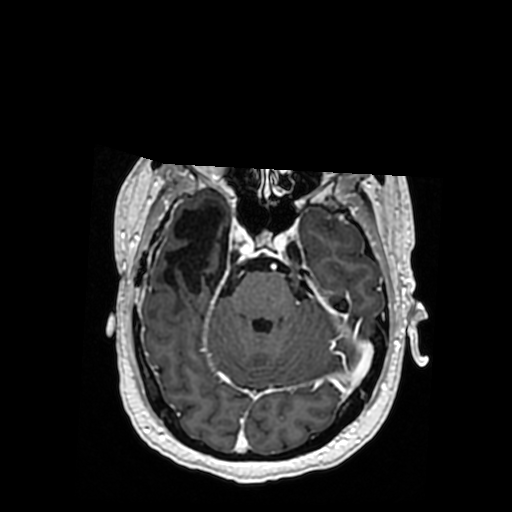
Brain MRI from a brain-tumour surgery series, one axial slice. Slice 239 of 364 in the series (ordered by position). T1-weighted post-contrast. 0.5 mm slice thickness. 512 × 512 image matrix, field of view 260 × 260 mm. Case-level facts recorded for this patient, not image findings: histopathology: Oligodendroglioma; WHO grade: 3; IDH mutation: yes; tumour location: Right Posterior Temporal Inferior Parietal.
Annotated regions visible in this slice (outlined manually by an expert reader):
- previous resection cavity: box from (x=165, y=207) to (x=228, y=295) px